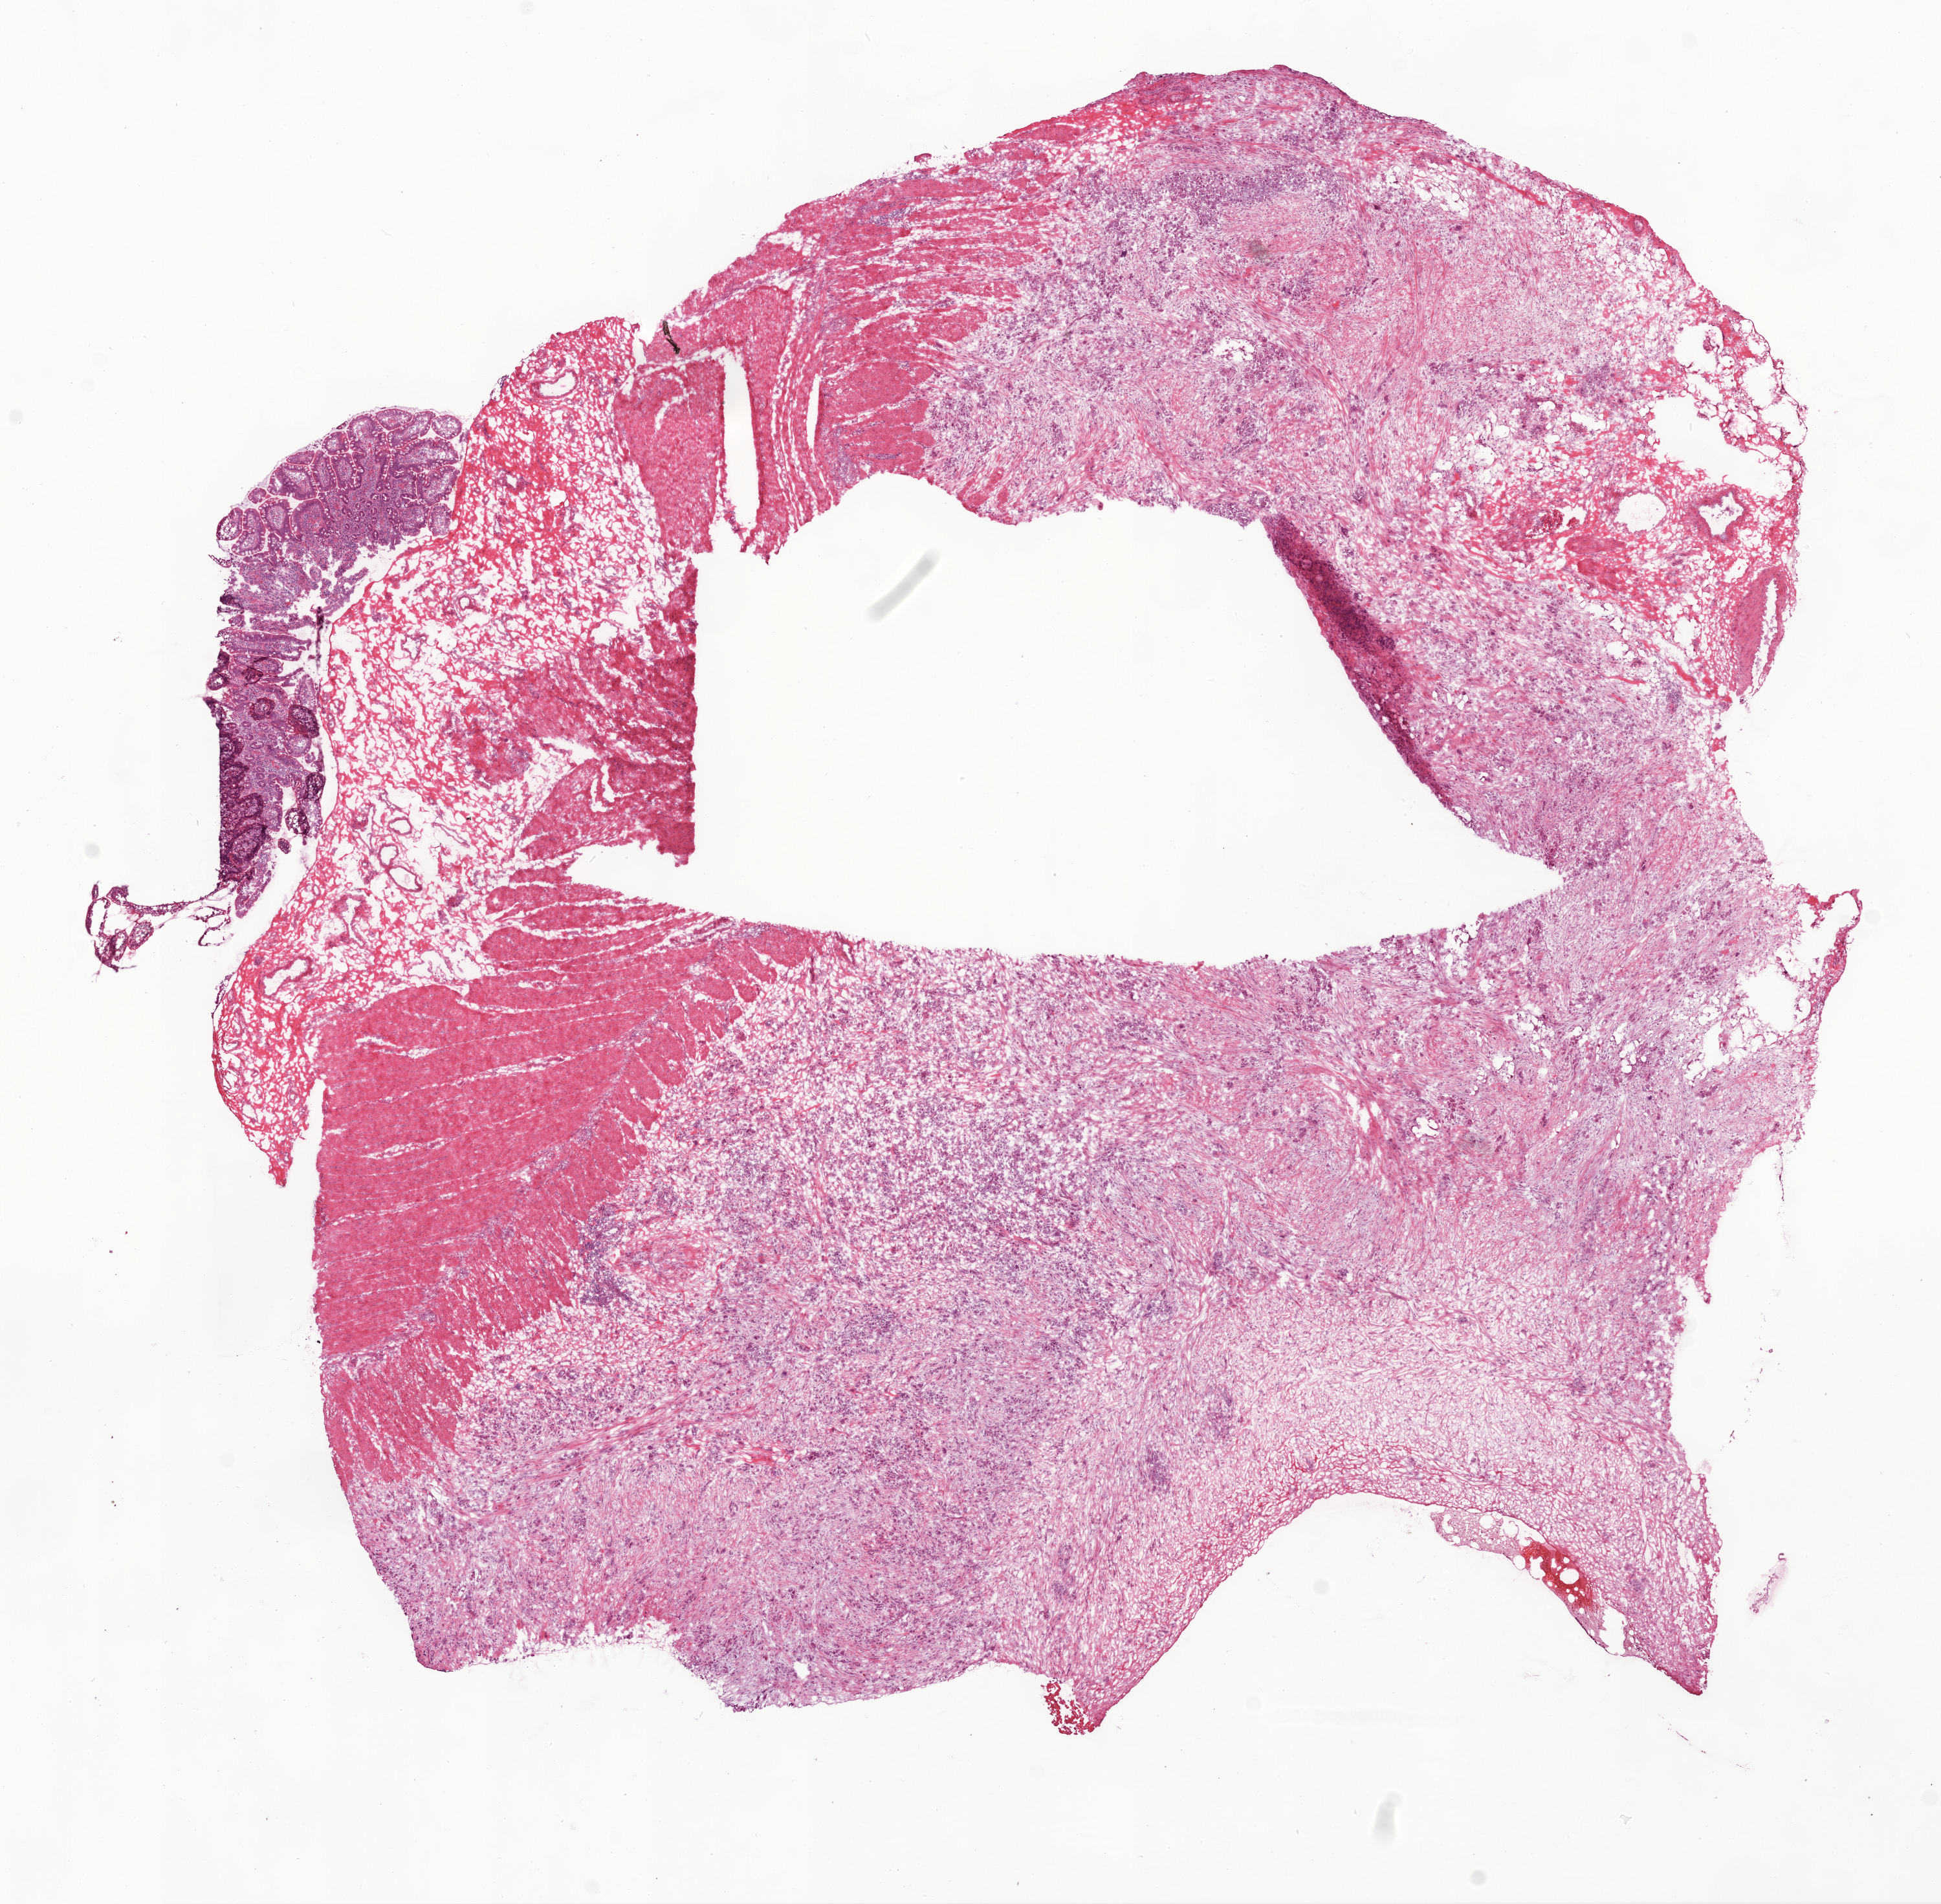
Digitized H&E-stained tissue section (whole slide), low-resolution overview of the scanned area, about 12.0 x 11.8 mm (acquisition: 20x scan), frozen section from the bottom of the tissue portion, ovary, recurrent tumour sample. Female, age 40 years at initial diagnosis. Slide review estimates, as recorded: tumour cells 60%, tumour nuclei 80%, normal cells 20%, stromal cells 20%, necrosis 0%.
• this section: recurrent tumour
• patient diagnosis: Serous cystadenocarcinoma, NOS